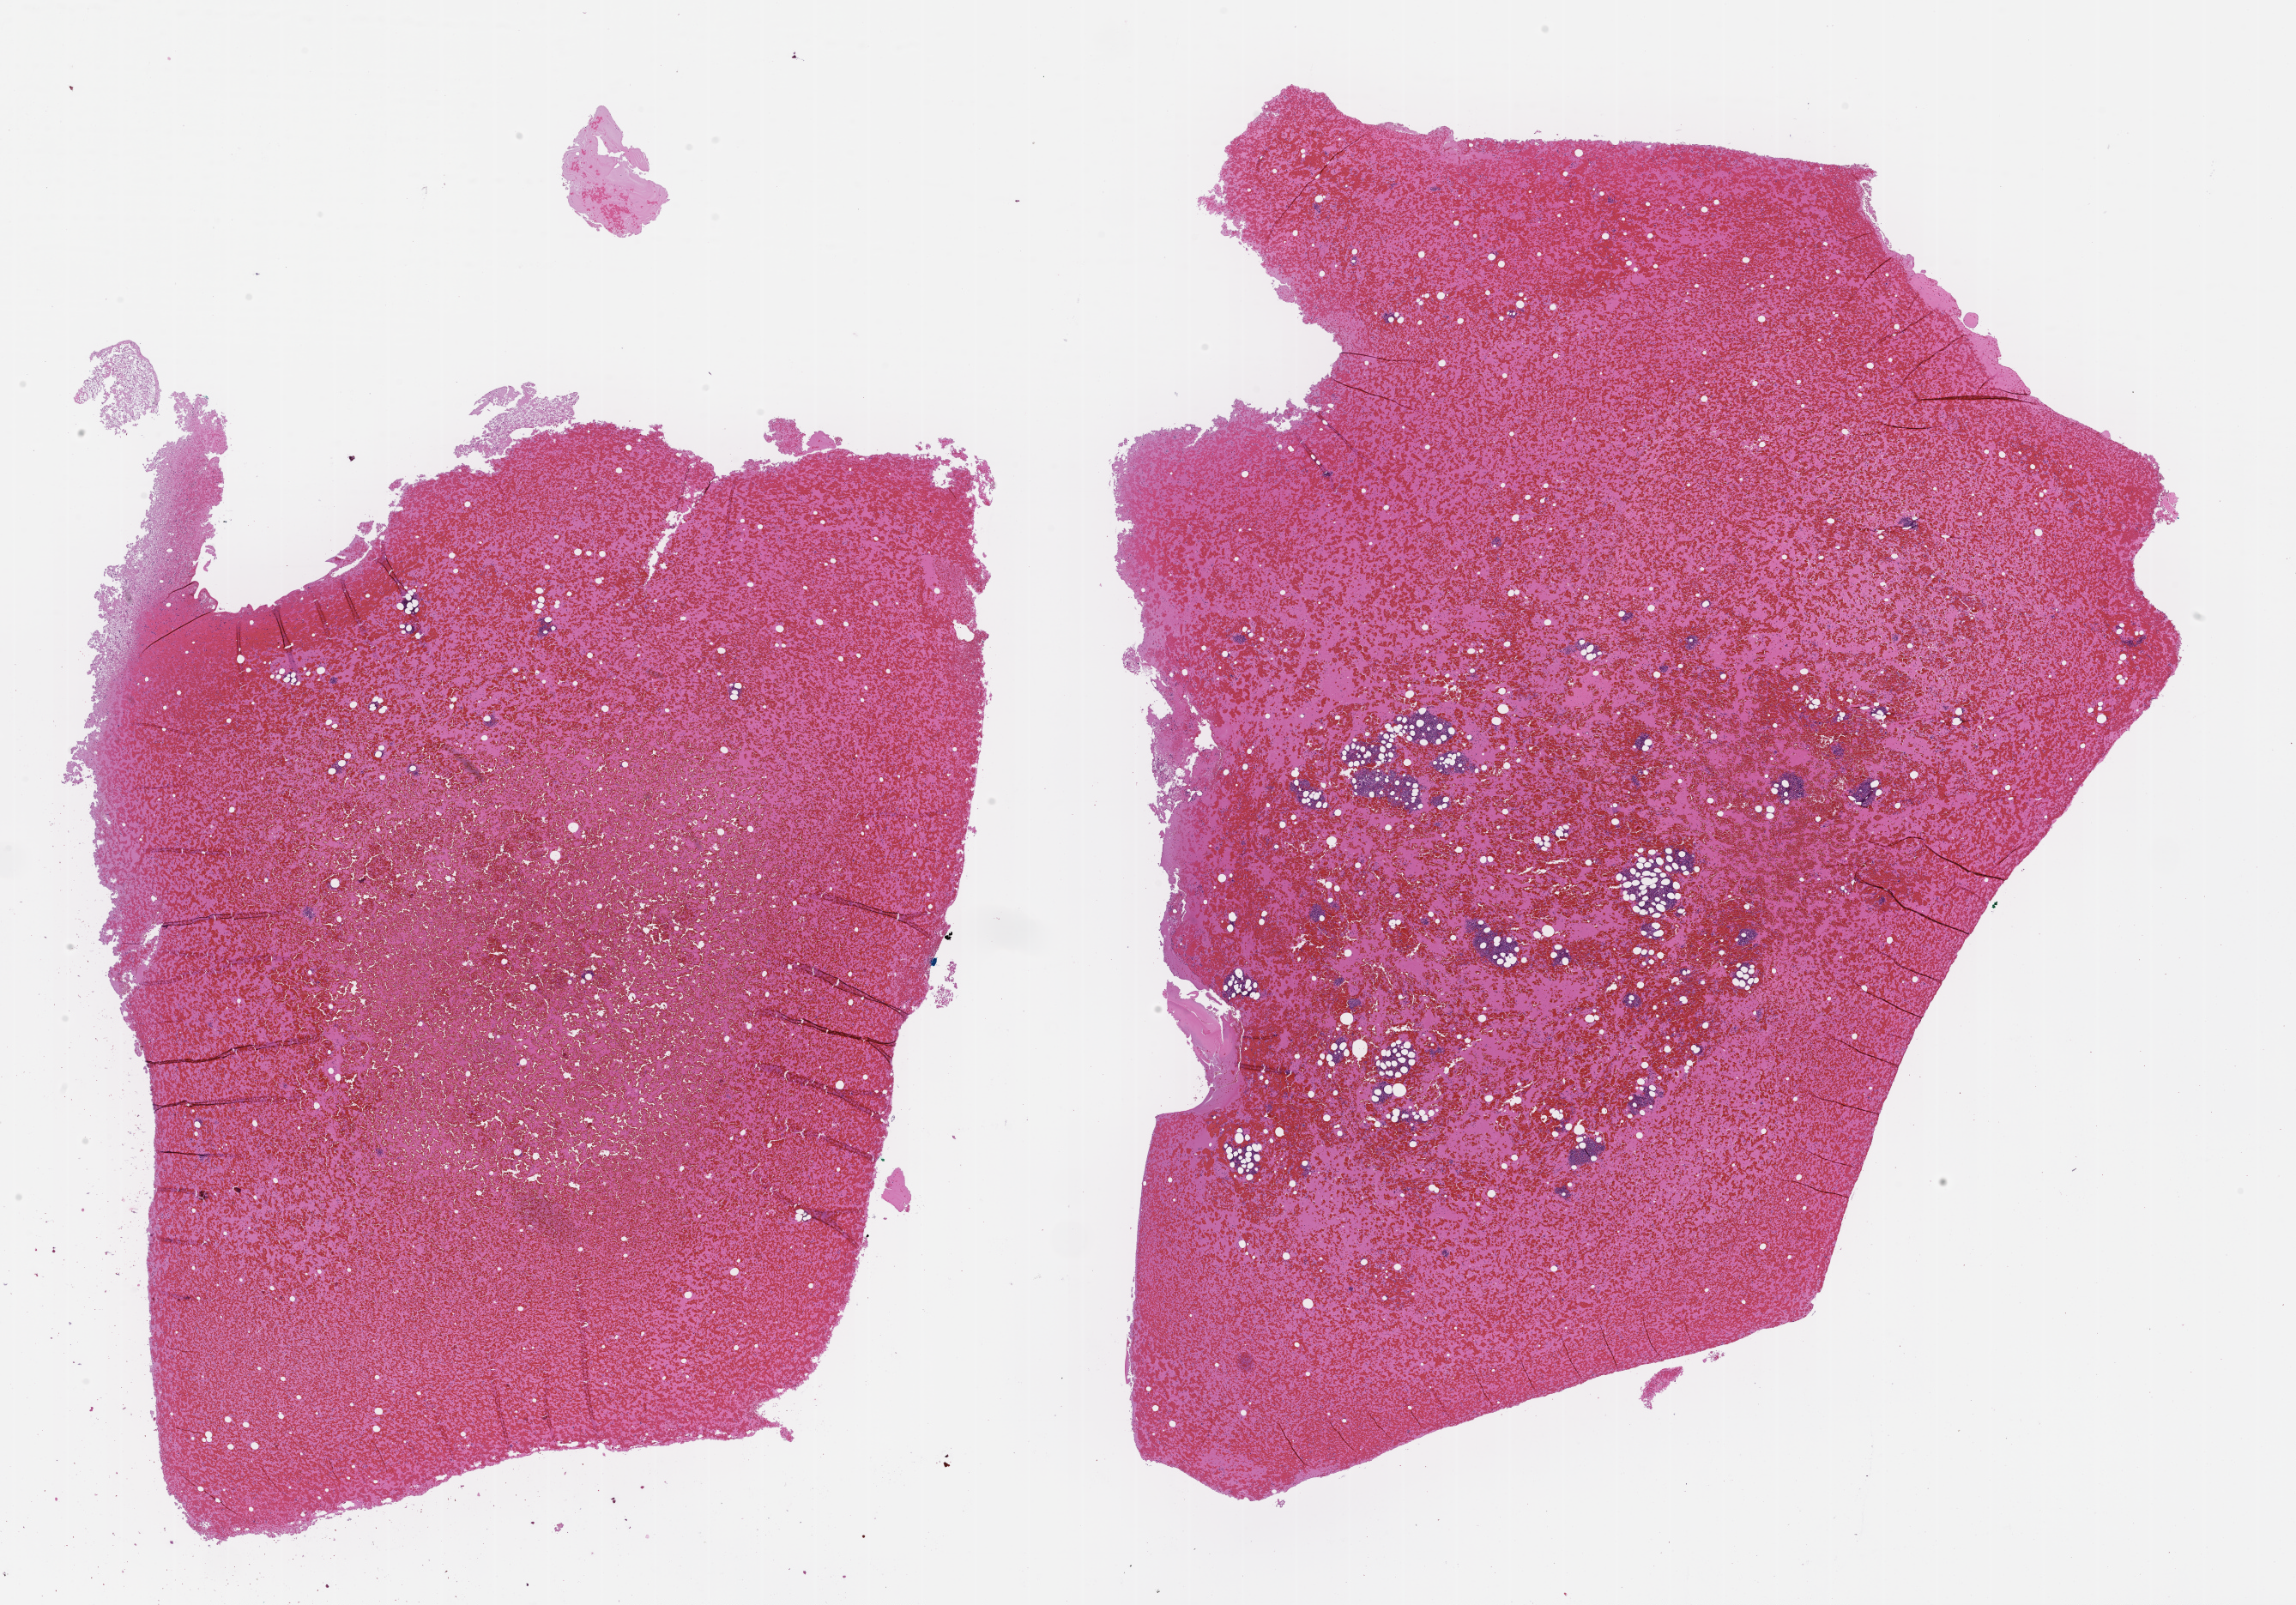
Whole-slide image, haematoxylin and eosin stain — a low-resolution overview of the entire scanned area, about 21.6 x 15.1 mm. Formalin-fixed paraffin-embedded section. Site: bone marrow. Patient sex: male.
This section: primary tumour tissue. Diagnosis: Plasma Cell Myeloma.